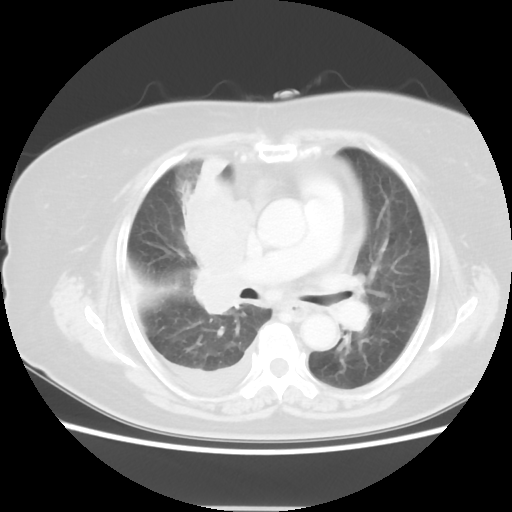
Chest CT, one axial slice; reconstruction kernel STANDARD; 120 kVp; lung window (W 1500 / L -600 HU); 5 mm slice thickness; 512 × 512 image matrix, field of view 360 × 360 mm. Female patient, age 73 years. From the clinical record (not read from this slice): clinical TNM (as recorded): T3 N3 M1b.
Structures marked on this image (rectangle marked by the reading radiologist):
- lung tumour (recorded histology: small cell carcinoma): box from (x=179, y=148) to (x=266, y=322) px